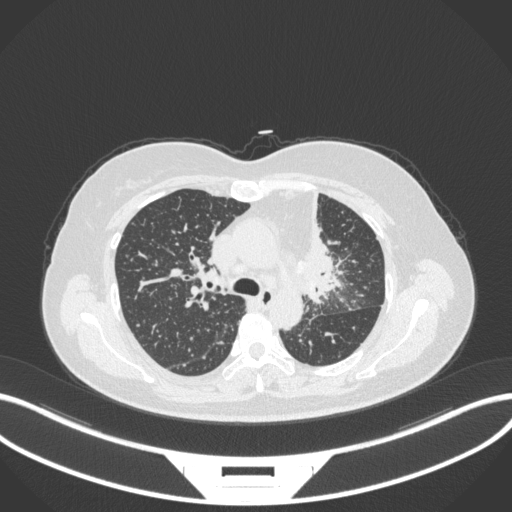
Chest CT, one axial slice; slice 225 of 348 in the series (ordered by position); lung window (W 1500 / L -600 HU); 512 × 512 image matrix. Female patient, age 49 years. From the clinical record (not read from this slice): clinical TNM (as recorded): T1c N0 M1.
Annotated regions visible in this slice (bounding box drawn by a radiologist):
- lung tumour (recorded histology: adenocarcinoma): bounding box (x1, y1, x2, y2) in pixels: (295, 183, 343, 310)